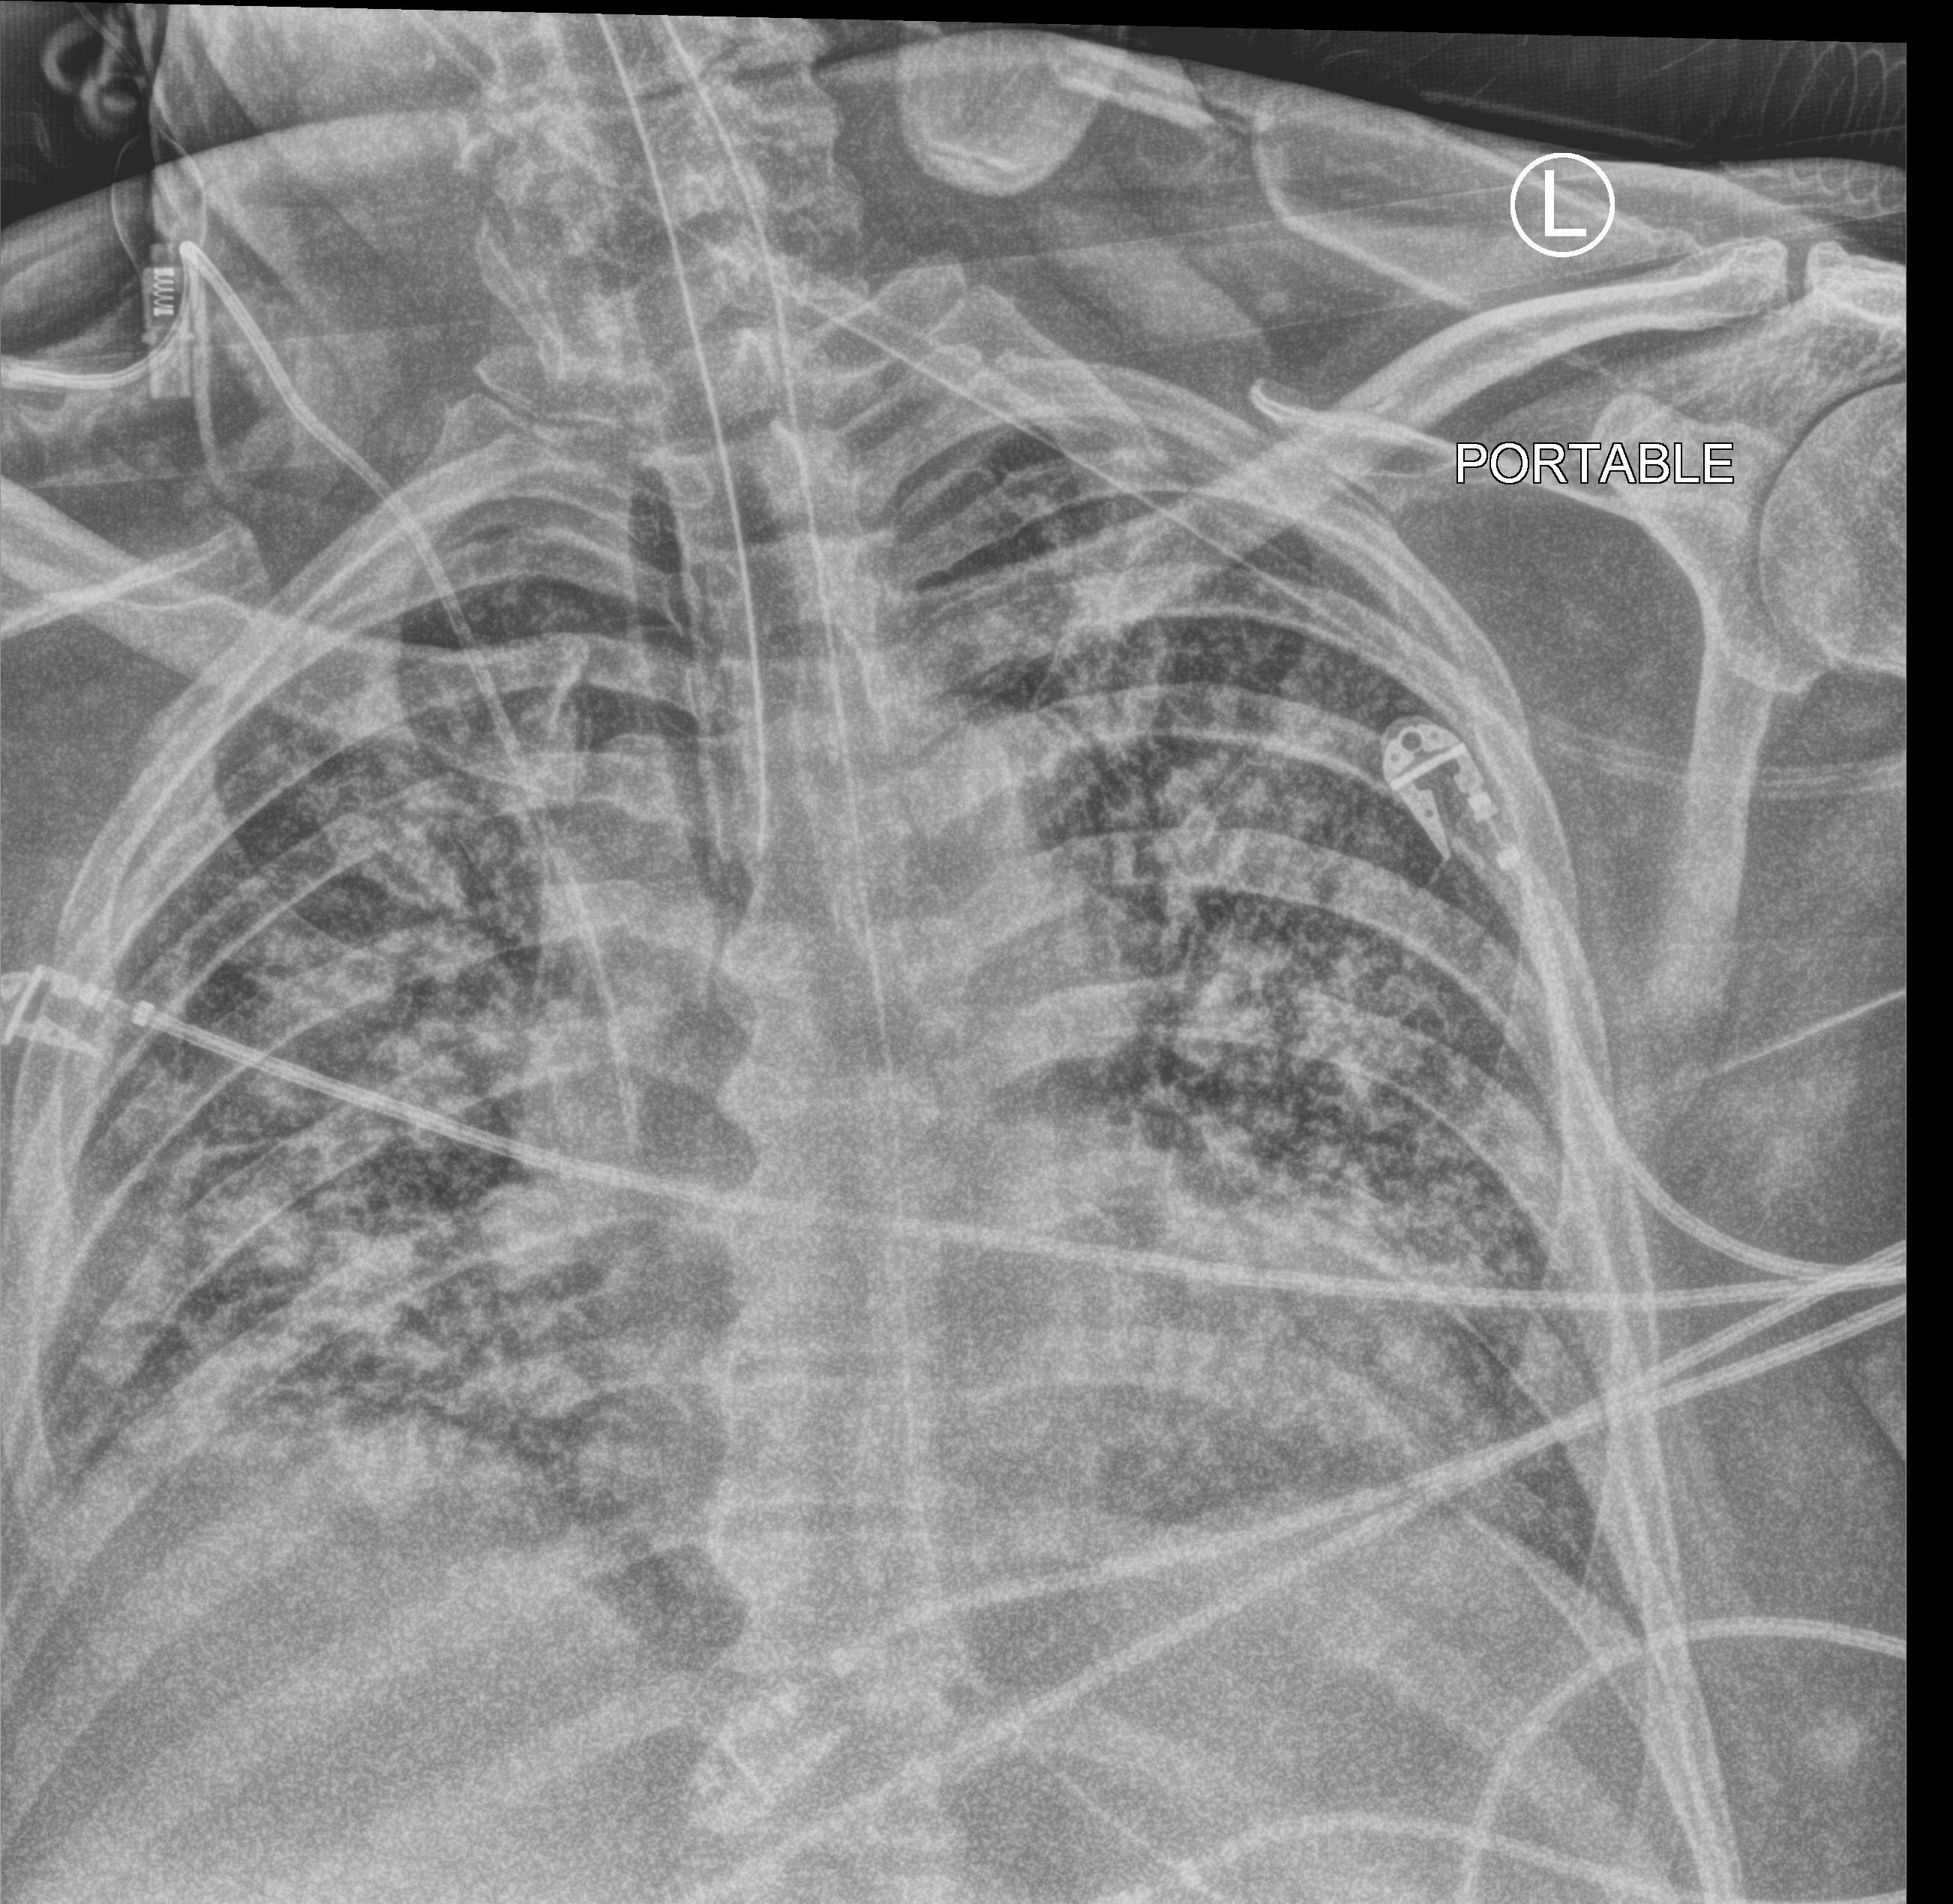
Portable chest radiograph, anteroposterior (AP) projection. Male patient hospitalised with COVID-19, age 60–74 years.
Admission-level facts for this patient (not findings on this image; timing relative to this image not recorded):
- admitted to intensive care during this hospital stay: yes